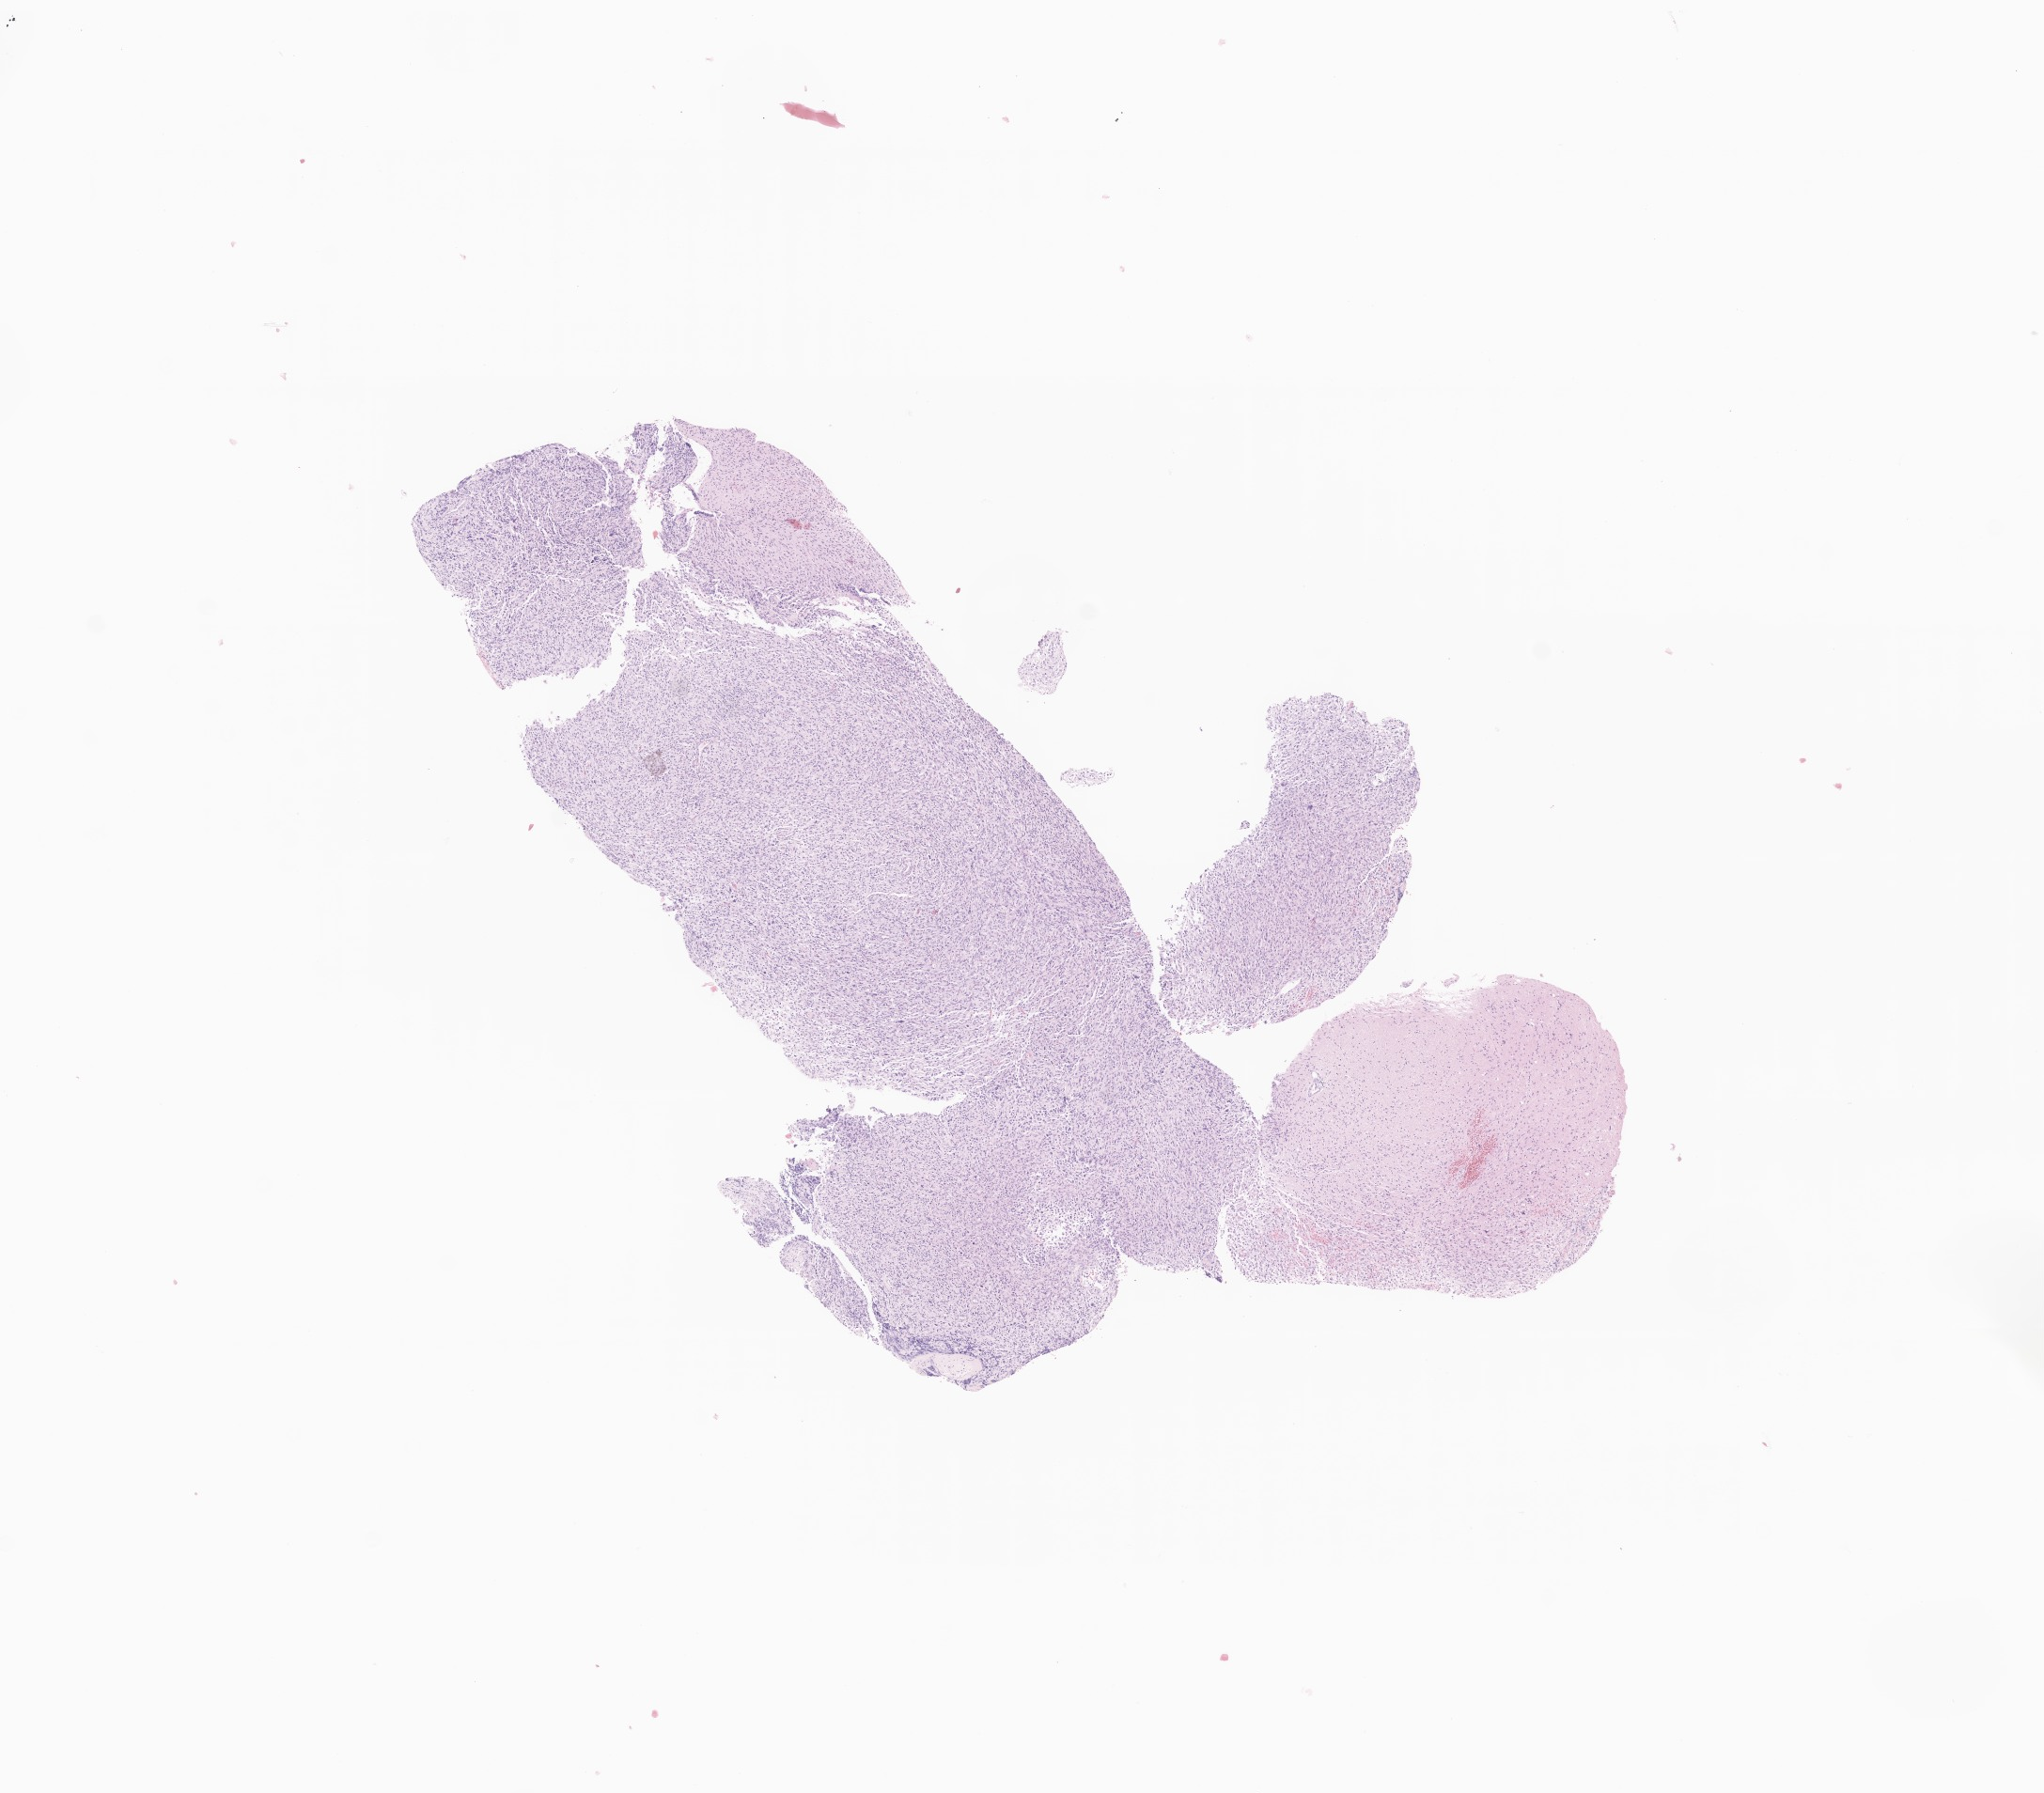
Haematoxylin and eosin whole-slide image of tumor tissue from the frontal lobe — a low-resolution overview of the entire scanned area, about 9.2 x 8.0 mm. Formalin-fixed, paraffin-embedded (FFPE) tissue. Male patient, age 169 months (14 years 1 month).
* diagnosis (ICD-O-3 morphology term): Astrocytoma, NOS